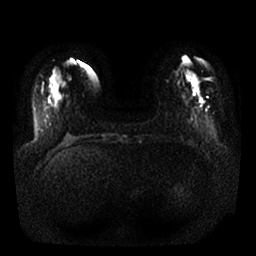
Breast MRI, one axial slice; slice 5 of 25 in the series (ordered by position); diffusion-weighted series; image 2 of 4 stored at this slice position (different b-values; order by instance number); 1.5 T; 256 × 256 image matrix, field of view 340 × 340 mm. Female patient.
Outlined on this slice (outlined manually by an expert reader):
- tumour on diffusion-weighted imaging: bounding box [x1, y1, x2, y2] px = [200, 100, 203, 104]